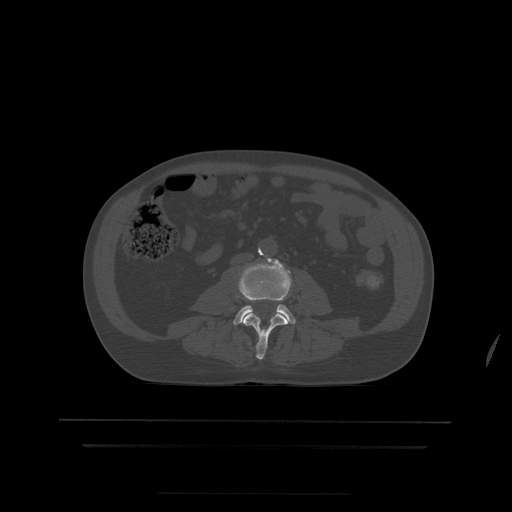
CT including the spine, one axial slice. Position 108 of 522 along the scan axis. Bone window (W 1800 / L 400 HU). 1.25 mm slice thickness. 512 × 512 image matrix. Patient age 68 years. Case-level facts recorded for this patient, not image findings: primary cancer: urothelial.
Outlined on this slice (semi-automatic segmentation, software-assisted and operator-edited):
- L3 vertebra: bounding box [x1, y1, x2, y2] px = [236, 296, 289, 360]
- L4 vertebra: [234, 258, 296, 325]